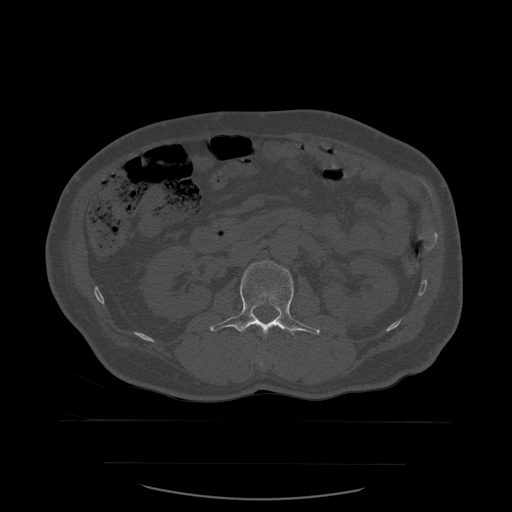
CT including the spine, one axial slice; position 222 of 590 along the scan axis; bone window (W 1800 / L 400 HU); 1.25 mm slice thickness; 512 × 512 image matrix, field of view 479 × 479 mm. Patient age 71 years. Case-level facts recorded for this patient, not image findings: primary cancer: lung.
Annotated regions visible in this slice (semi-automatic segmentation, software-assisted and operator-edited):
- L1 vertebra: bounding box (x1, y1, x2, y2) in pixels: (260, 352, 265, 366)
- L2 vertebra: (210, 261, 321, 335)